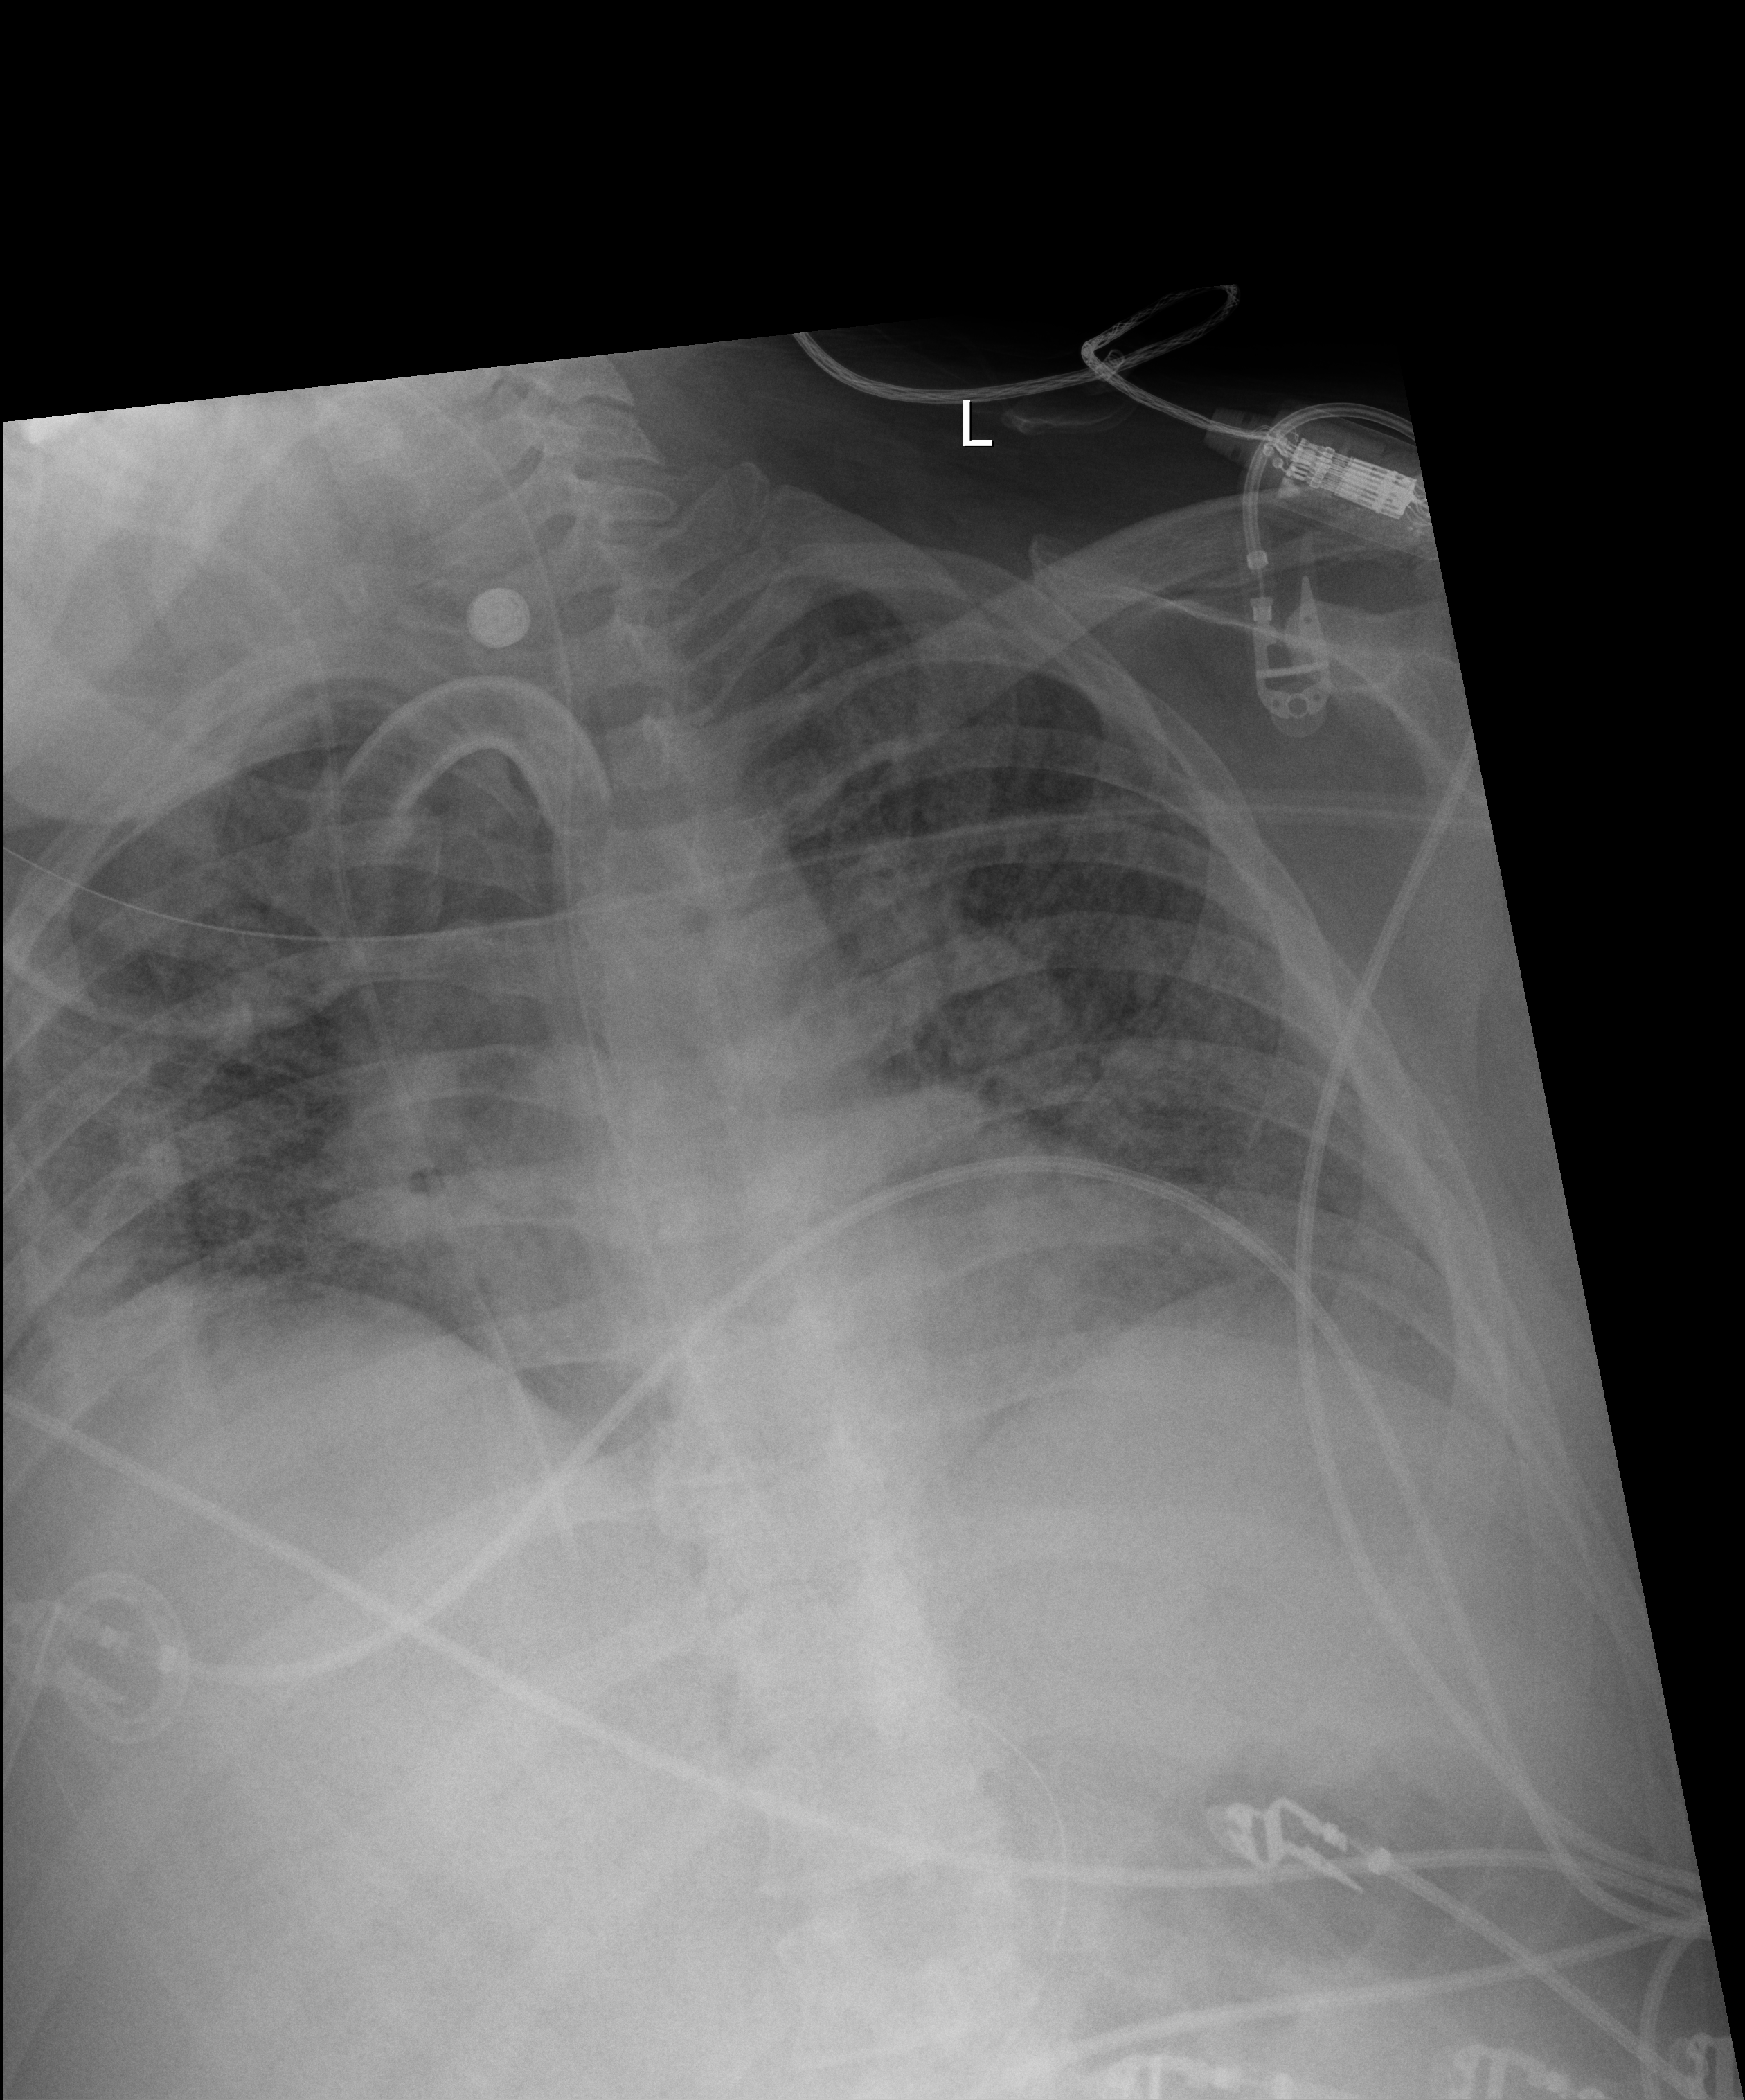
Portable chest radiograph, anteroposterior (AP) projection. Patient hospitalised with COVID-19; male, aged 18–59 years.
Admission-level facts for this patient (not findings on this image; timing relative to this image not recorded): diabetes (admission record): no.